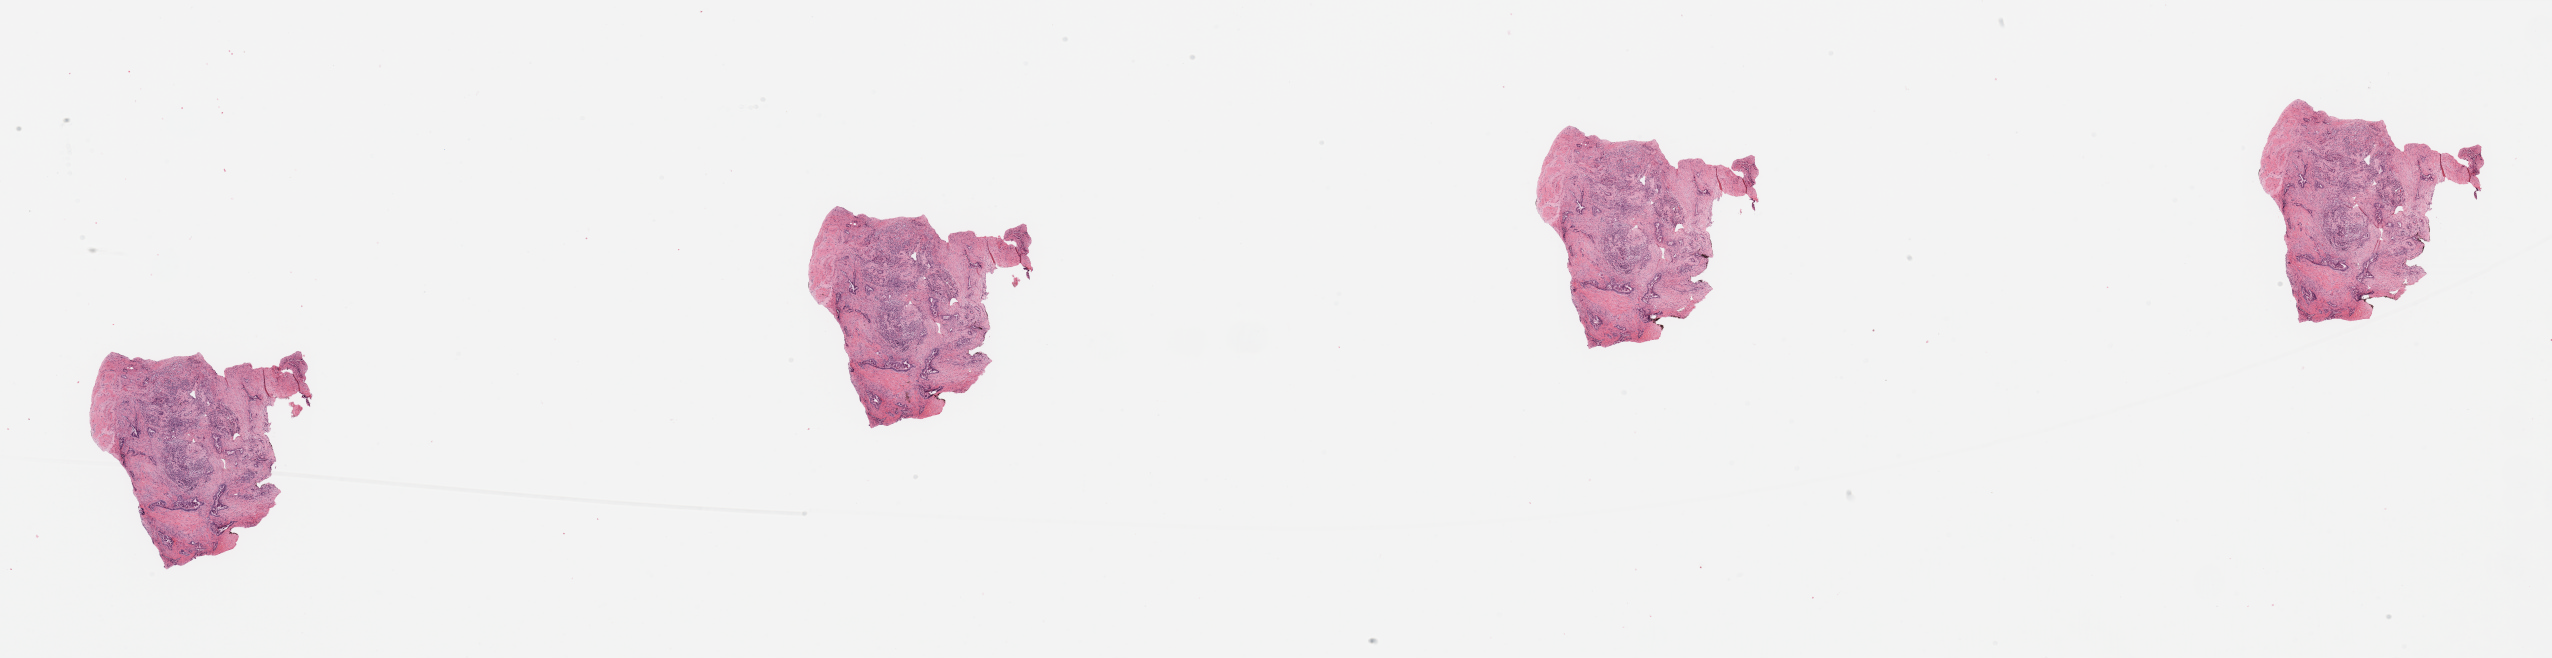
H&E-stained whole-slide image, shown as a low-resolution overview of the whole scanned area (about 40.4 x 10.4 mm). Tumour tissue sample, sampled site: pancreas. 80-year-old male patient. Slide review estimates, as recorded: tumour nuclei 30%, necrosis 0%.
Diagnosis: Infiltrating duct carcinoma, NOS.